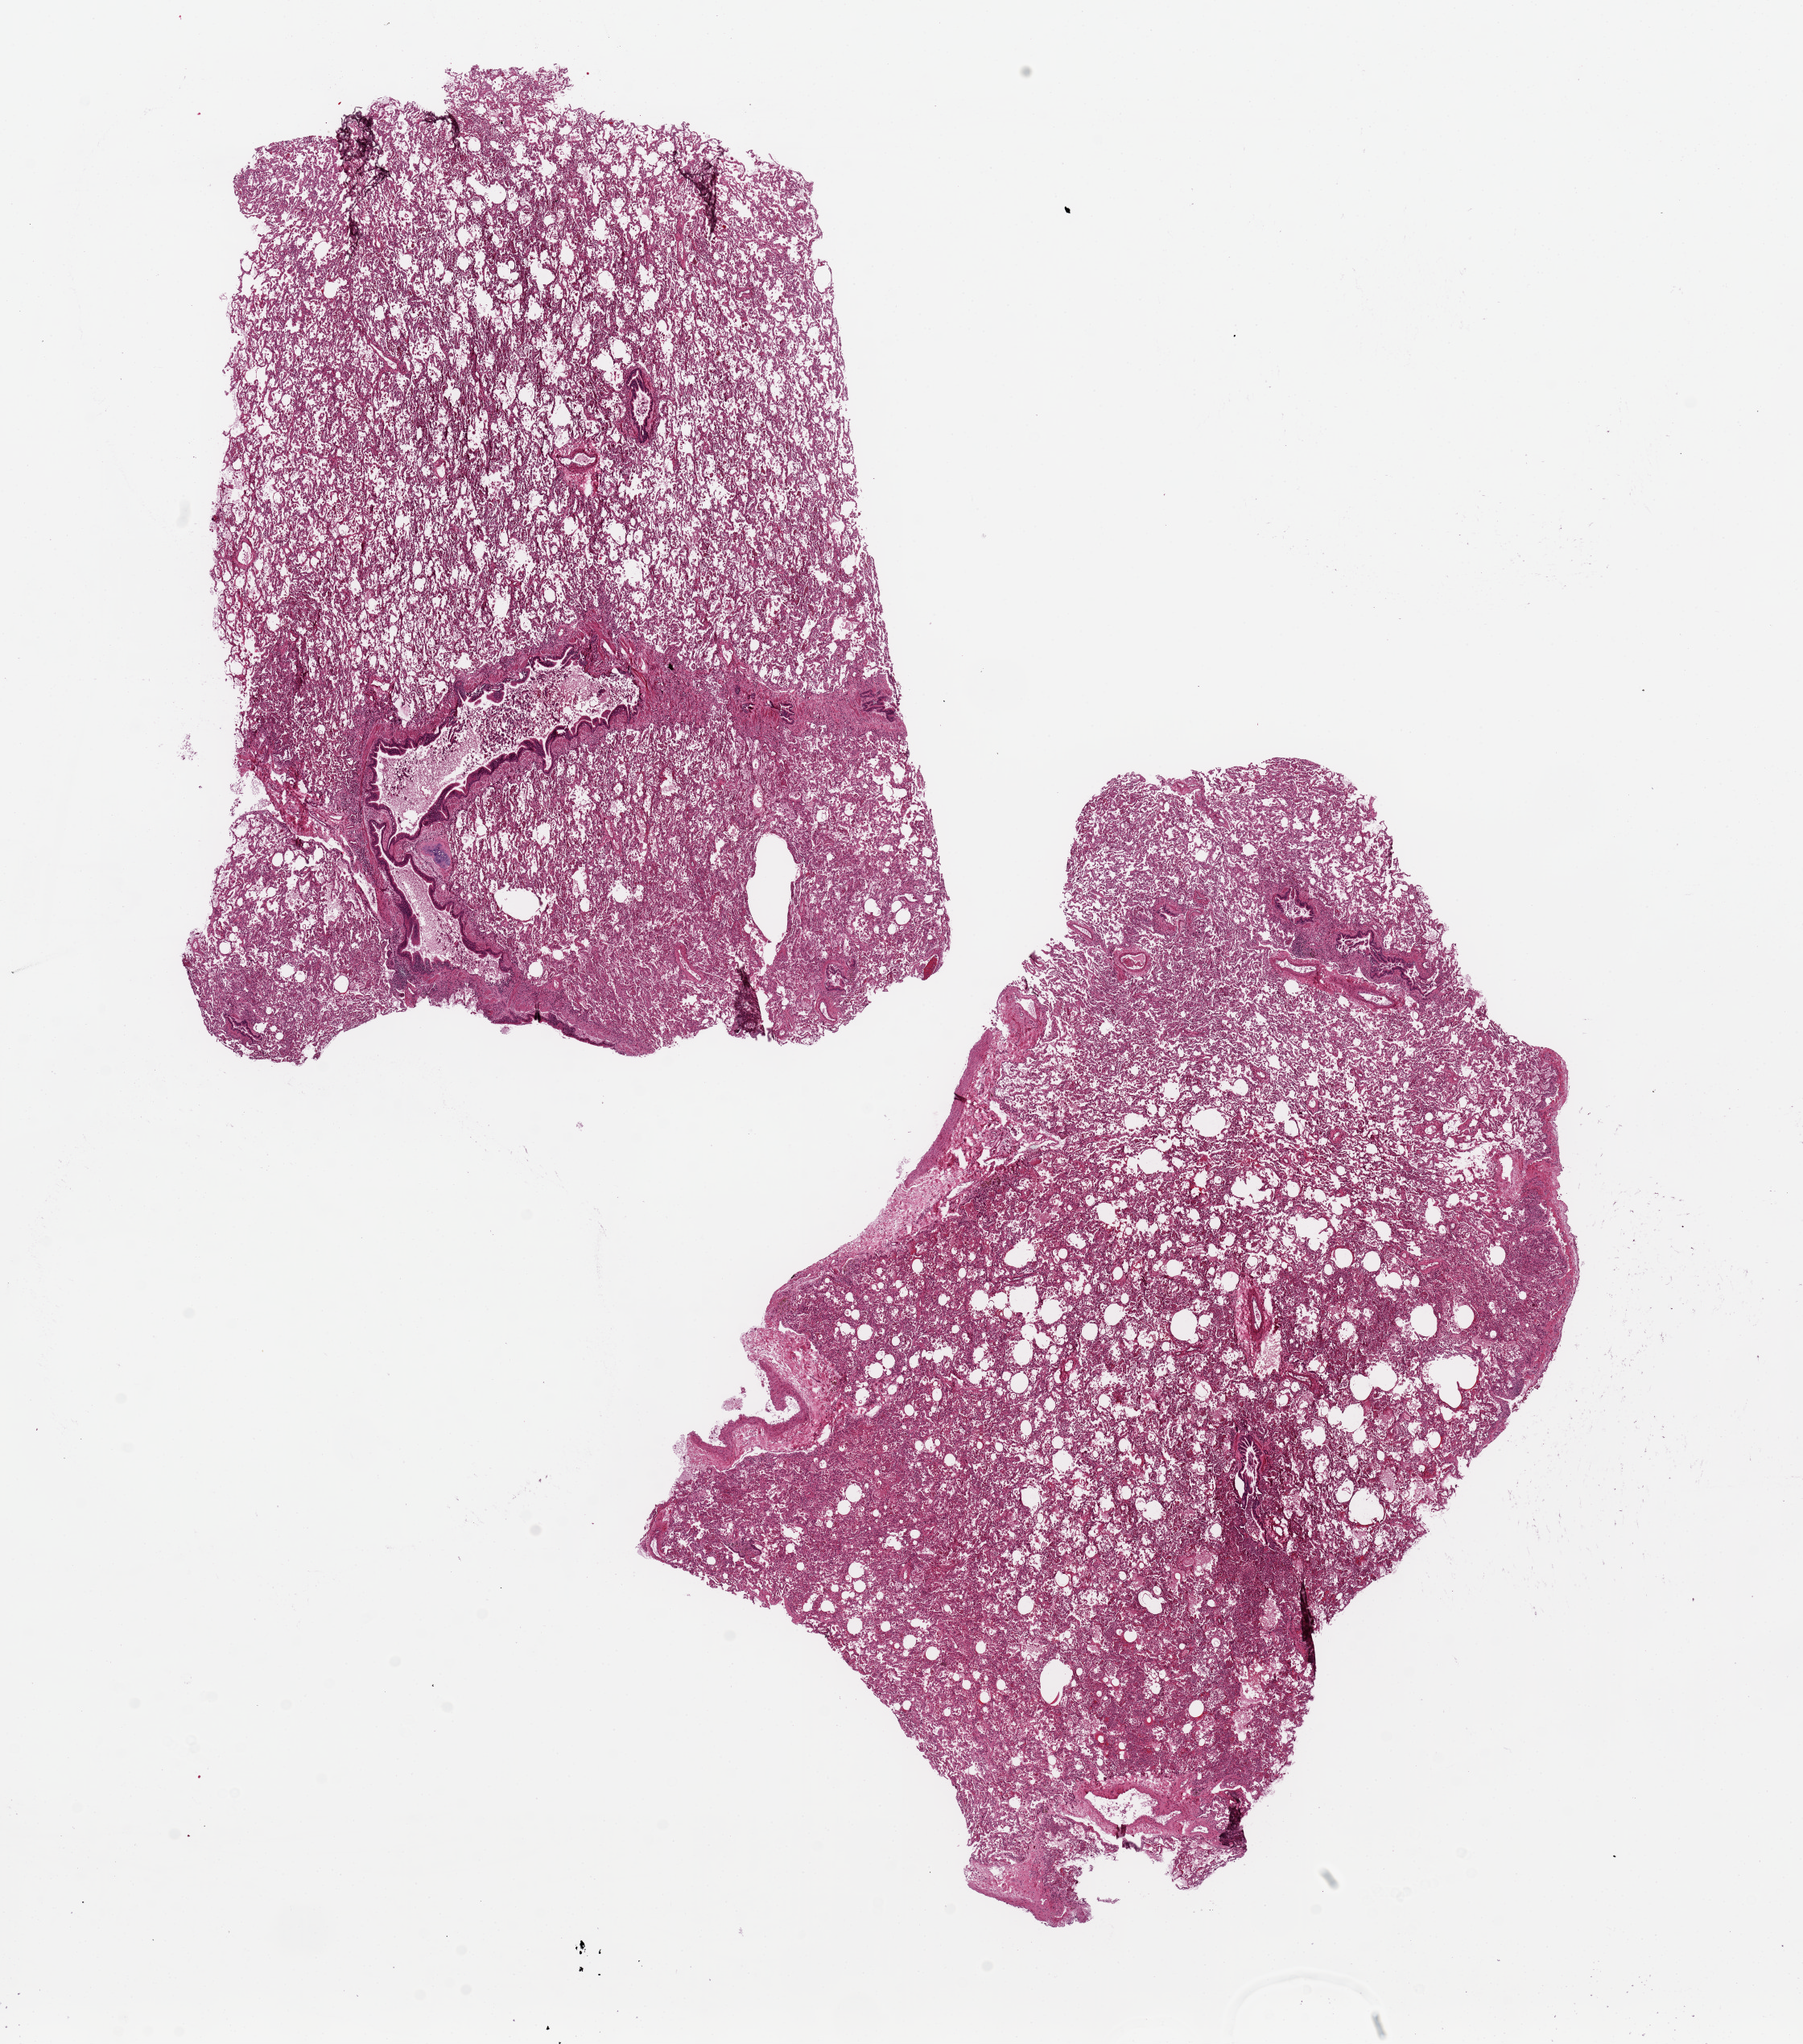
Haematoxylin and eosin whole-slide image, brightfield, shown as a low-resolution overview of the whole scanned area (about 17.7 x 20.1 mm). PAXgene-fixed, paraffin-embedded tissue. Sampled site (target tissue): lung. Donor tissue sample. Donor: male.
Review note (as recorded): 2 pieces, 10x7mm, patchy acute pneumonita/chronic pneumonitis.